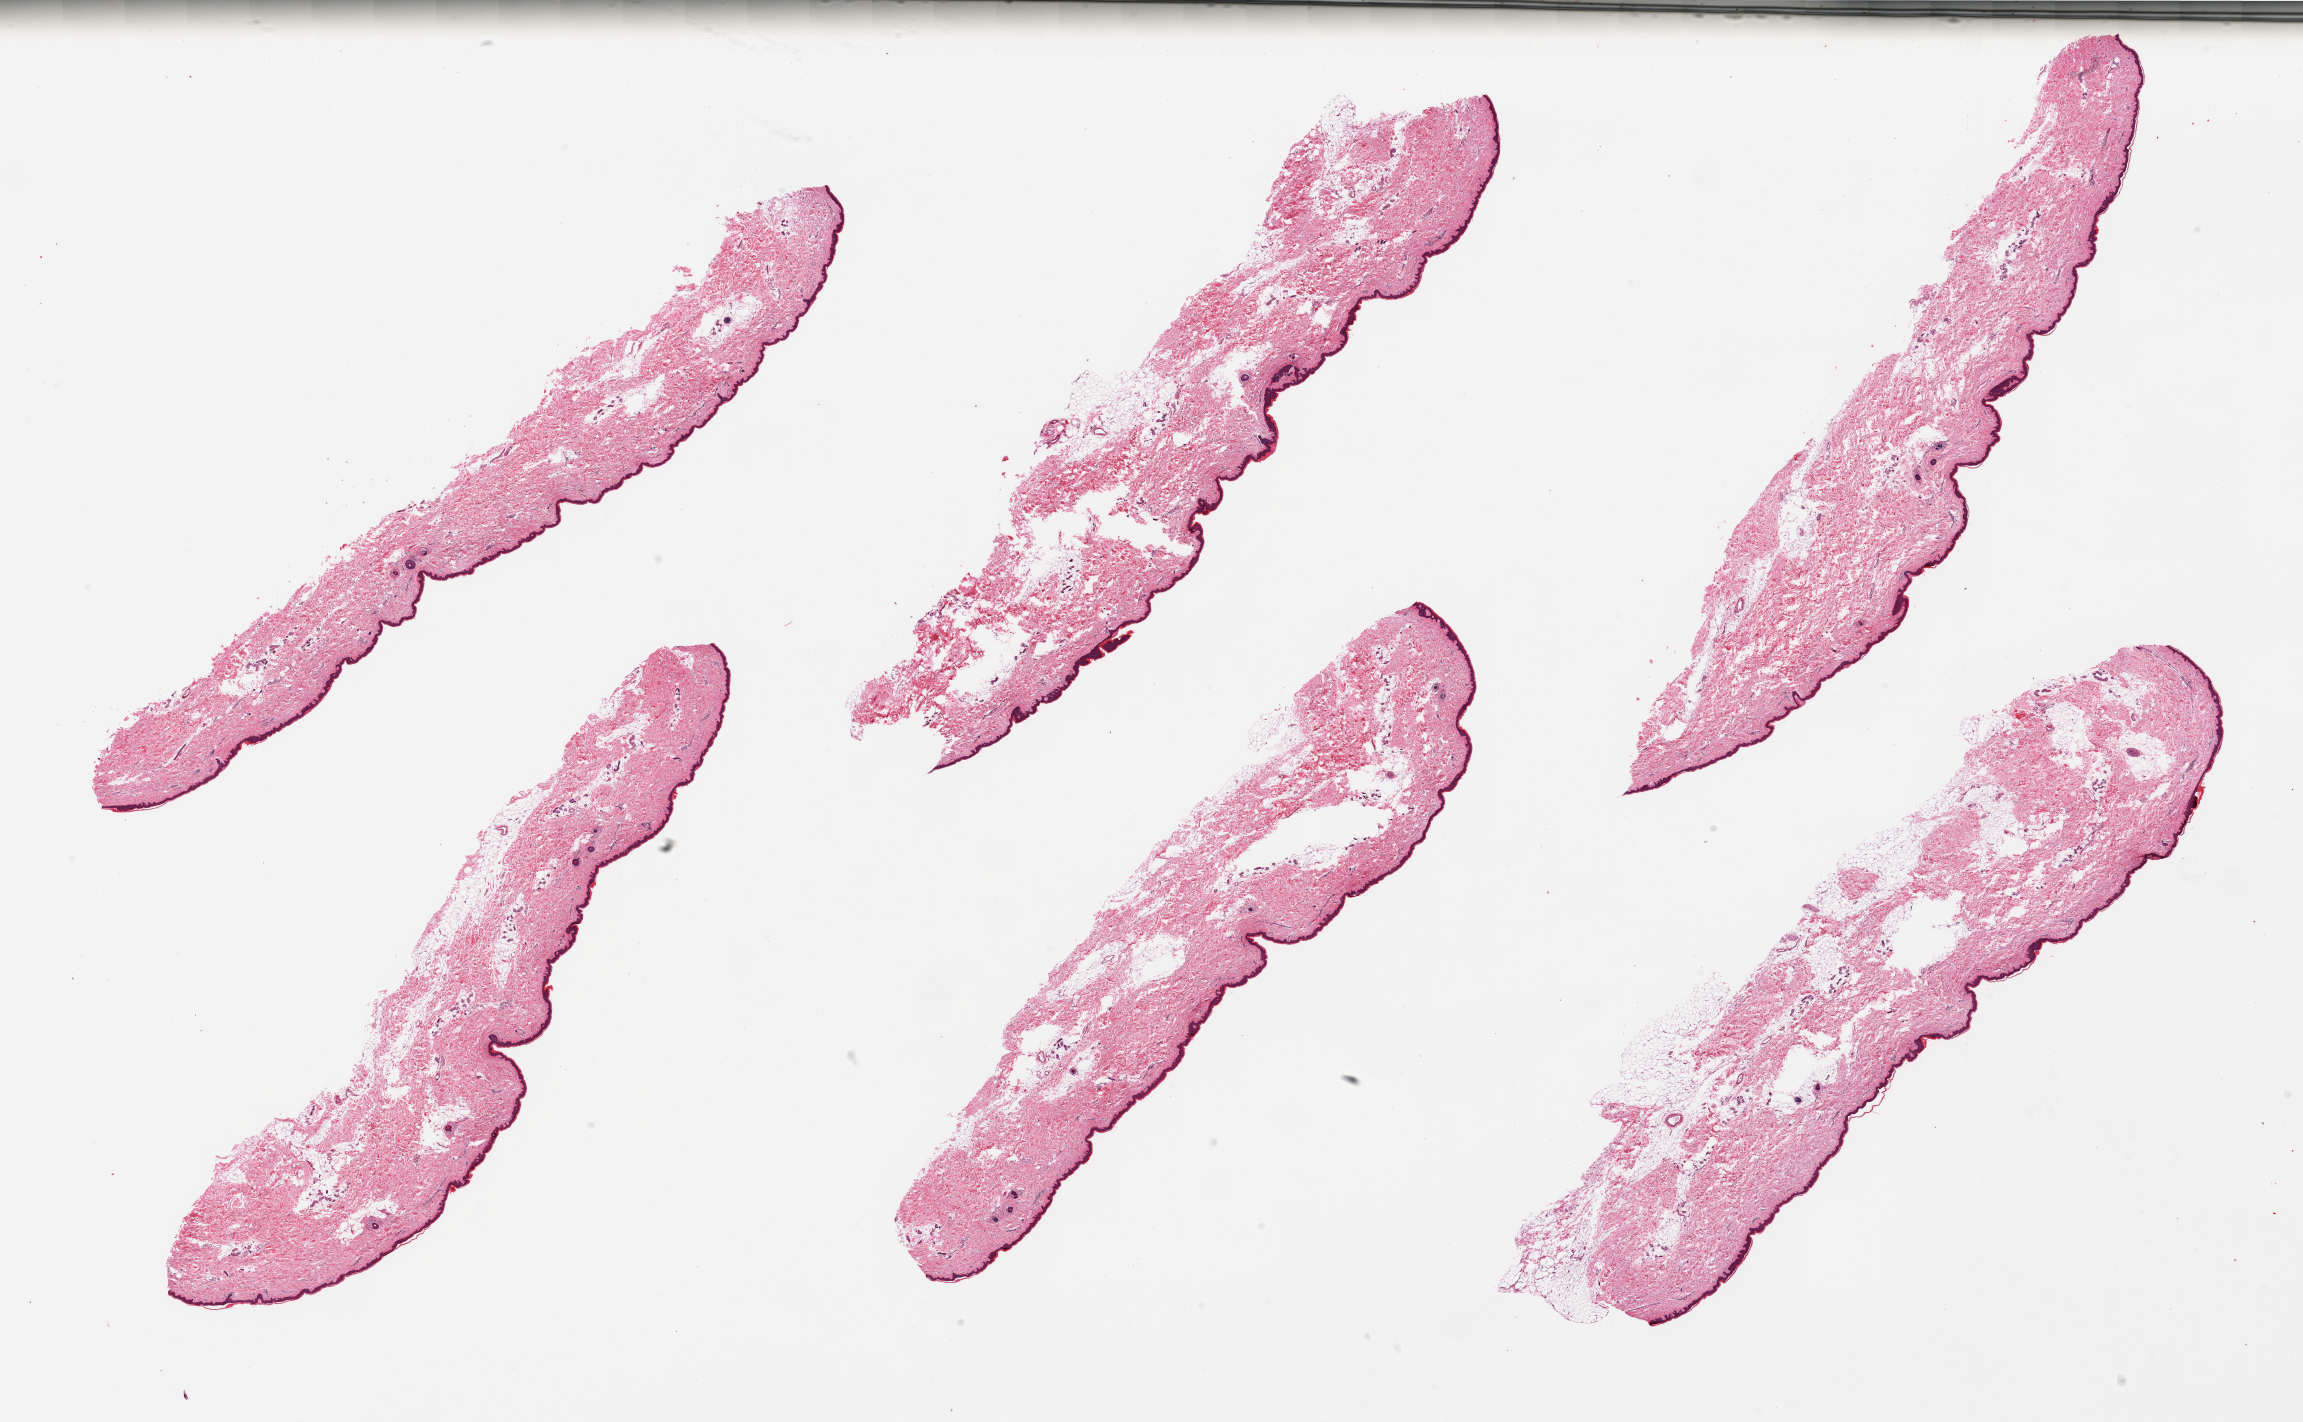
Whole-slide image, haematoxylin and eosin stain, whole scanned area (about 36.4 x 22.5 mm) shown as a low-resolution overview; PAXgene-fixed, paraffin-embedded tissue; section of skin of lower leg (target tissue); tissue donor sample. Female donor.
Pathologist's review note for this sample: 6 pieces, squamous epithelium is ~50 microns thick,, 2-3% total thickness; minimal dermal fat.